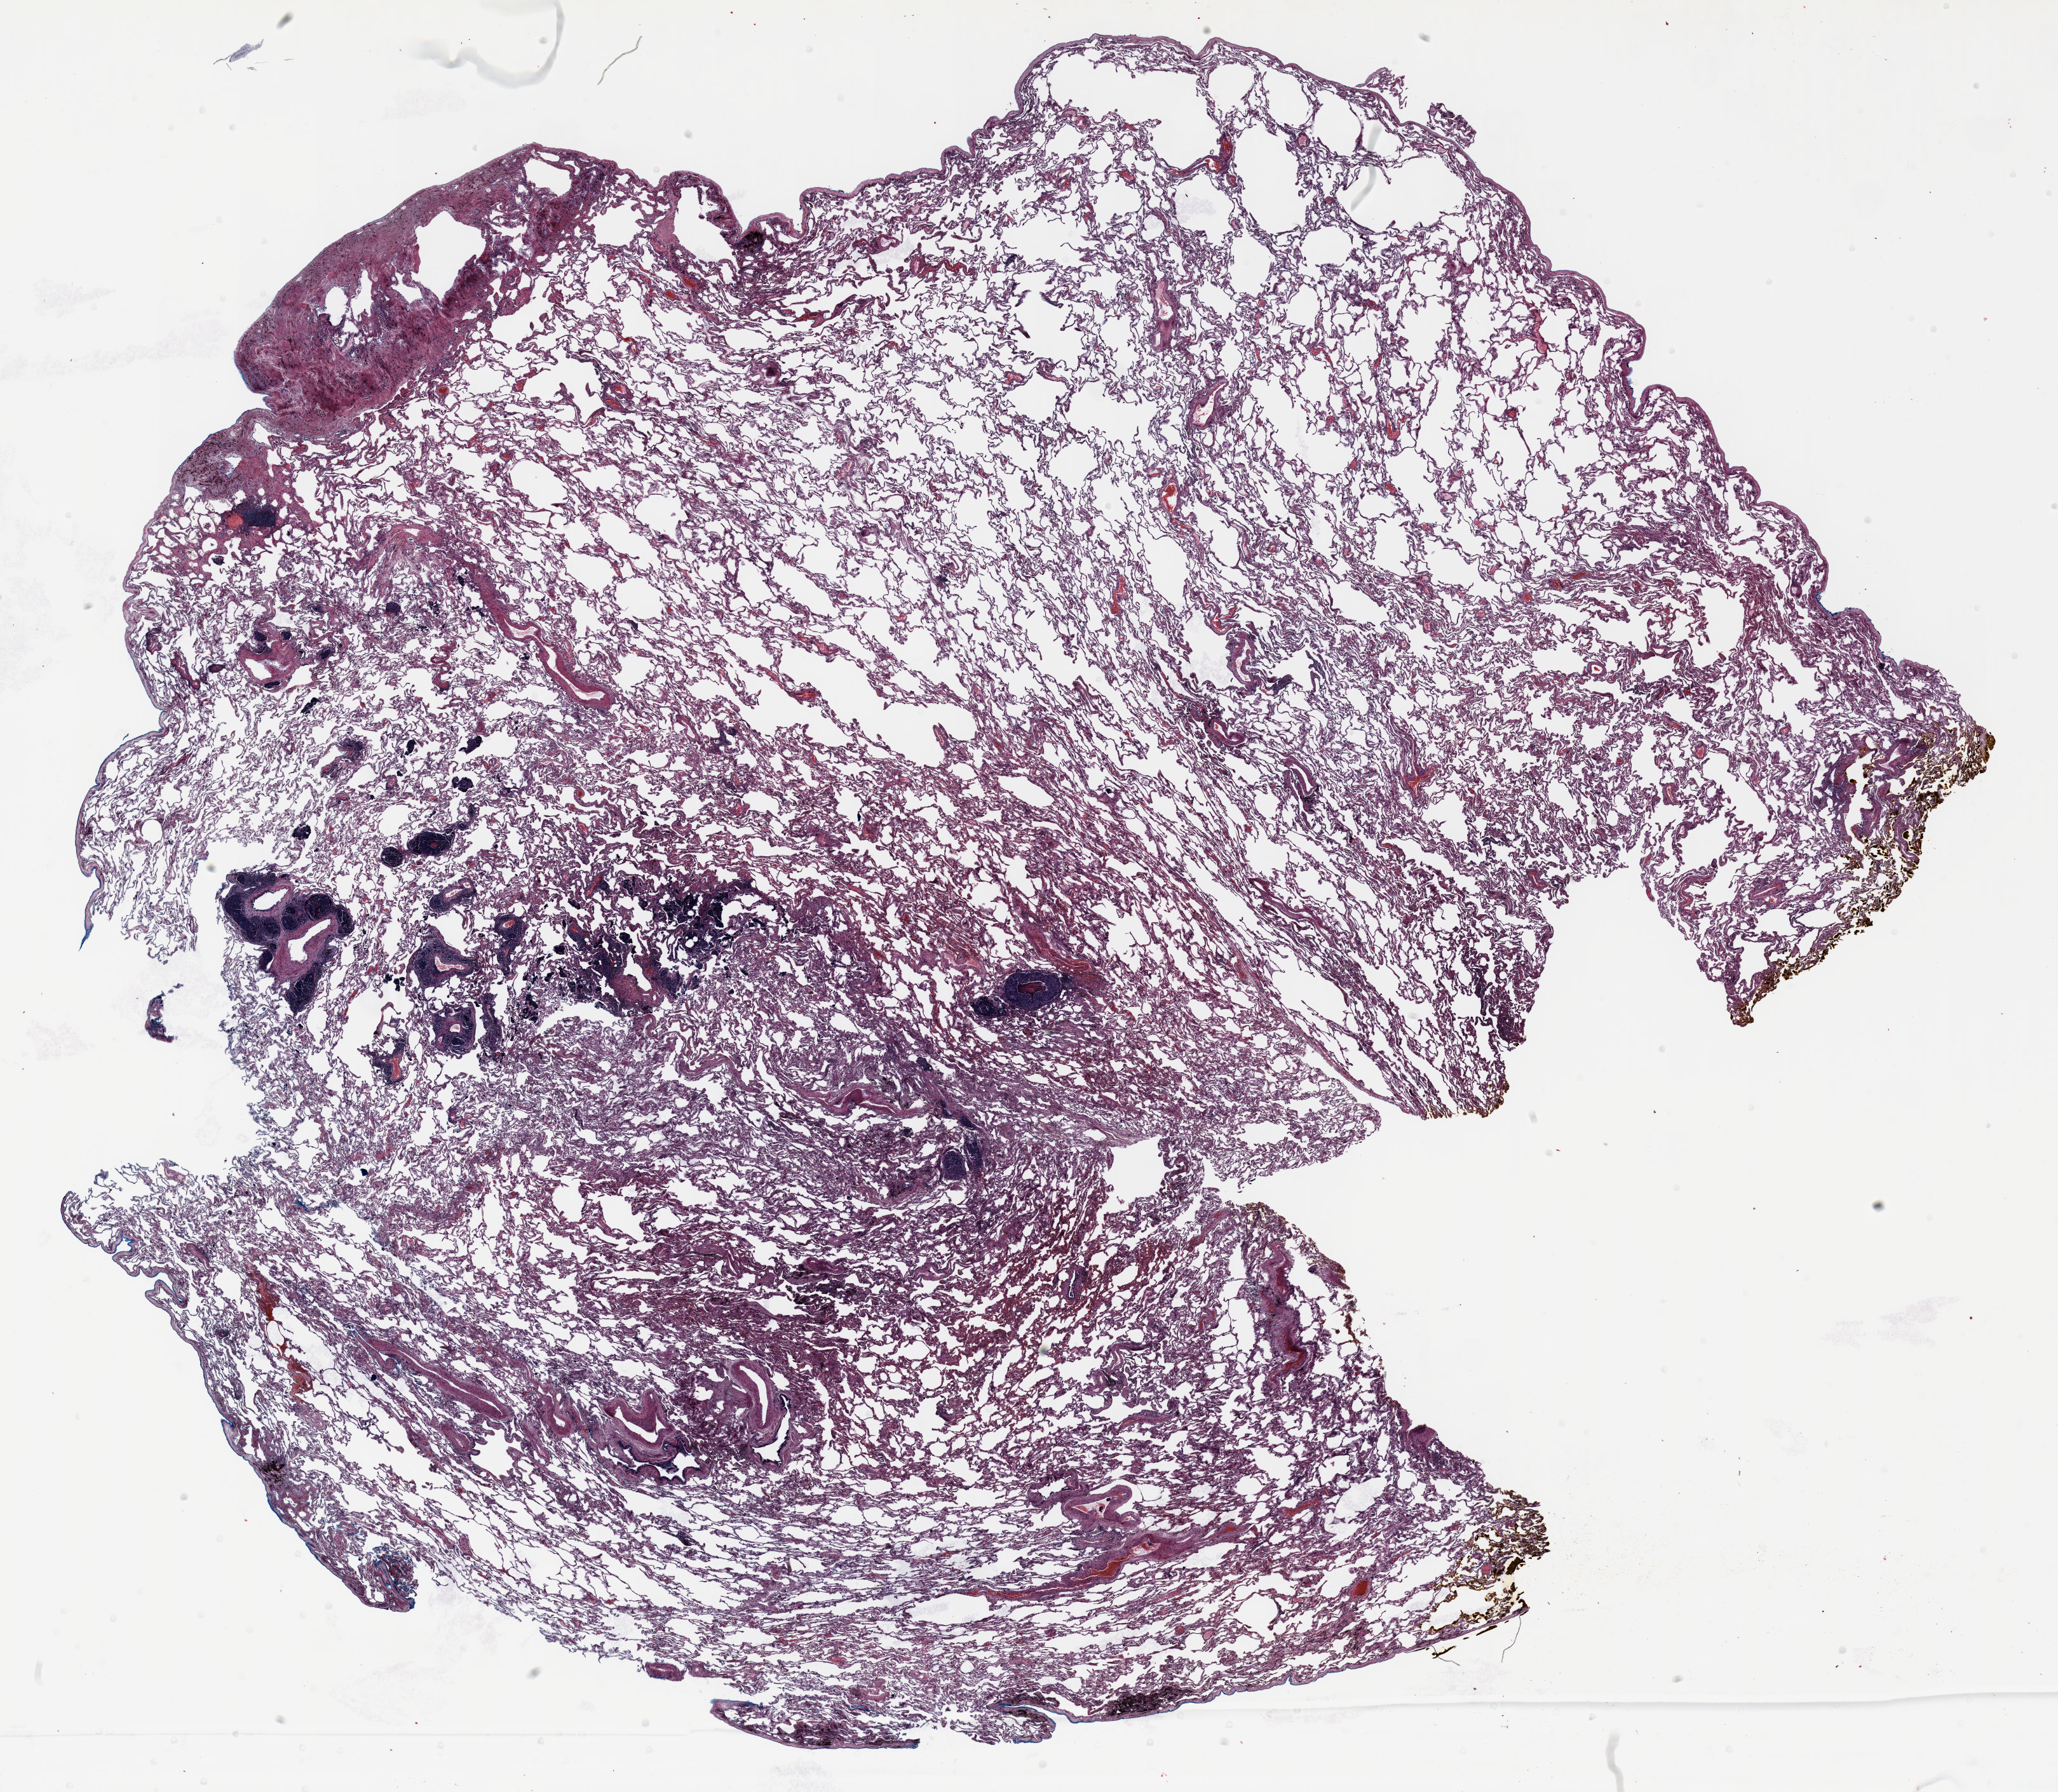
Whole-slide histology image, H&E, low-resolution overview of the scanned area, about 26.0 x 22.7 mm (from a 20x scan). Formalin-fixed paraffin-embedded (FFPE) section. Lung tissue. Male, age 67 at enrolment. Former smoker at enrolment. Grade: moderately differentiated (G2).
• ICD-O-3 topography: upper lobe of lung (C34.1)
• primary tumour location (clinical record): left upper lobe
• stage (AJCC 6th edition): IA
• participant's lung-cancer diagnosis: Atypical carcinoid tumor (ICD-O-3 8249/3)
• tumour size (pathology): 10 mm